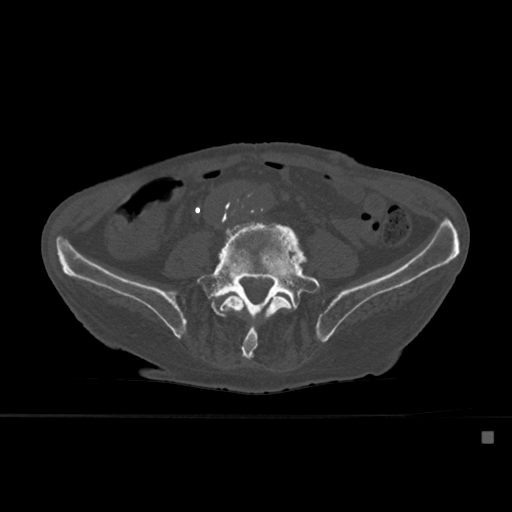
CT including the spine, one axial slice; slice 182 of 527 in the series (ordered by position); bone window (W 1800 / L 400 HU); 512 × 512 image matrix, field of view 373 × 373 mm. Male patient, age 78 years. From the clinical record (not read from this slice): primary cancer: prostate.
Structures marked on this image (semi-automatic segmentation, software-assisted and operator-edited):
- L4 vertebra: box from (x=220, y=291) to (x=295, y=362) px
- L5 vertebra: (x=197, y=227)–(x=321, y=326)